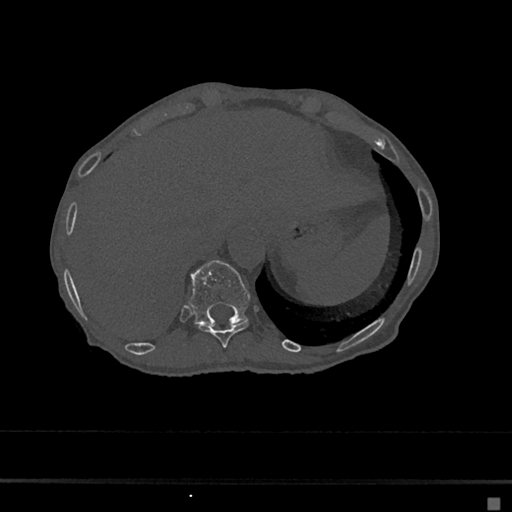
CT including the spine, one axial slice; position 199 of 797 along the scan axis; bone window (W 1800 / L 400 HU); 512 × 512 image matrix, field of view 360 × 360 mm. Patient: female, 68 years. Case-level facts recorded for this patient, not image findings: primary cancer: renal.
Annotated regions visible in this slice (semi-automatically segmented with operator editing):
- T10 vertebra: bounding box [x1, y1, x2, y2] px = [196, 321, 249, 348]
- T11 vertebra: [189, 260, 252, 324]